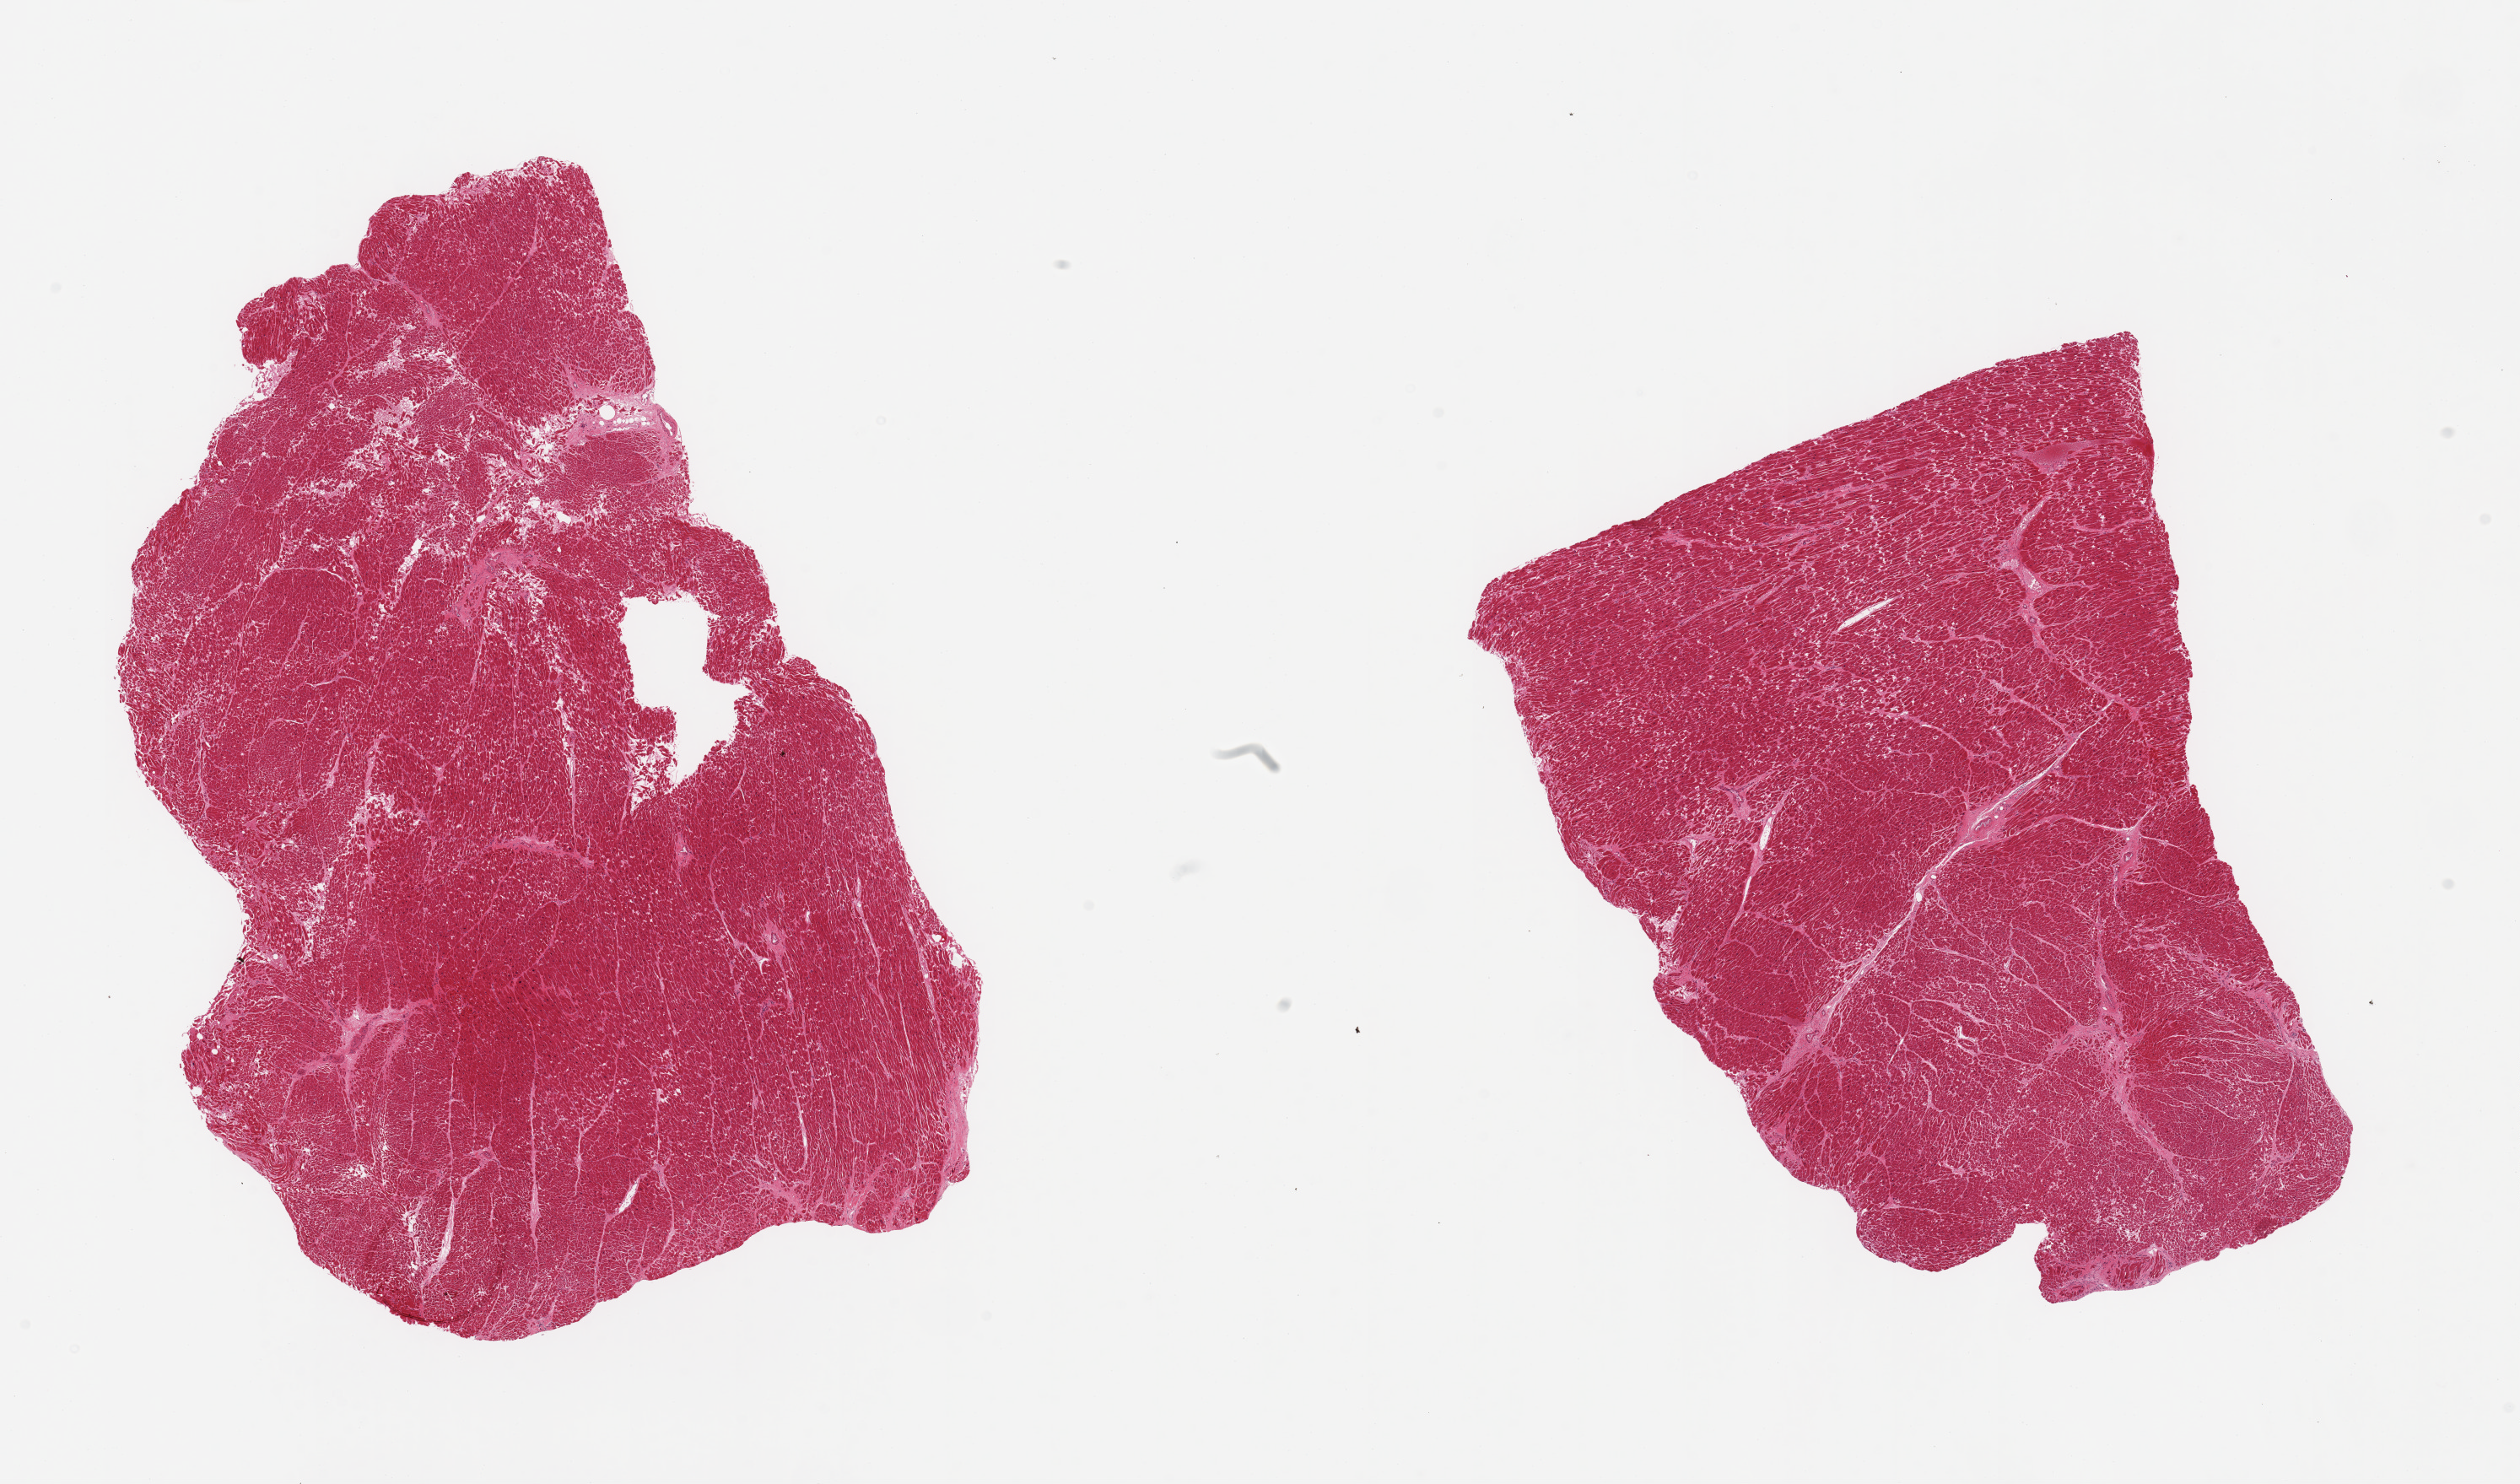
Haematoxylin and eosin whole-slide image, brightfield, a low-resolution overview of the entire scanned area, about 23.6 x 13.9 mm (from a 20x scan), PAXgene-fixed paraffin-embedded (PFPE) section, sampled site (target tissue): heart, donor tissue sample. Donor sex: female.
Pathologist's review note for this sample: 2 pieces; hypertrophied fibers; small focal hemorrhages.